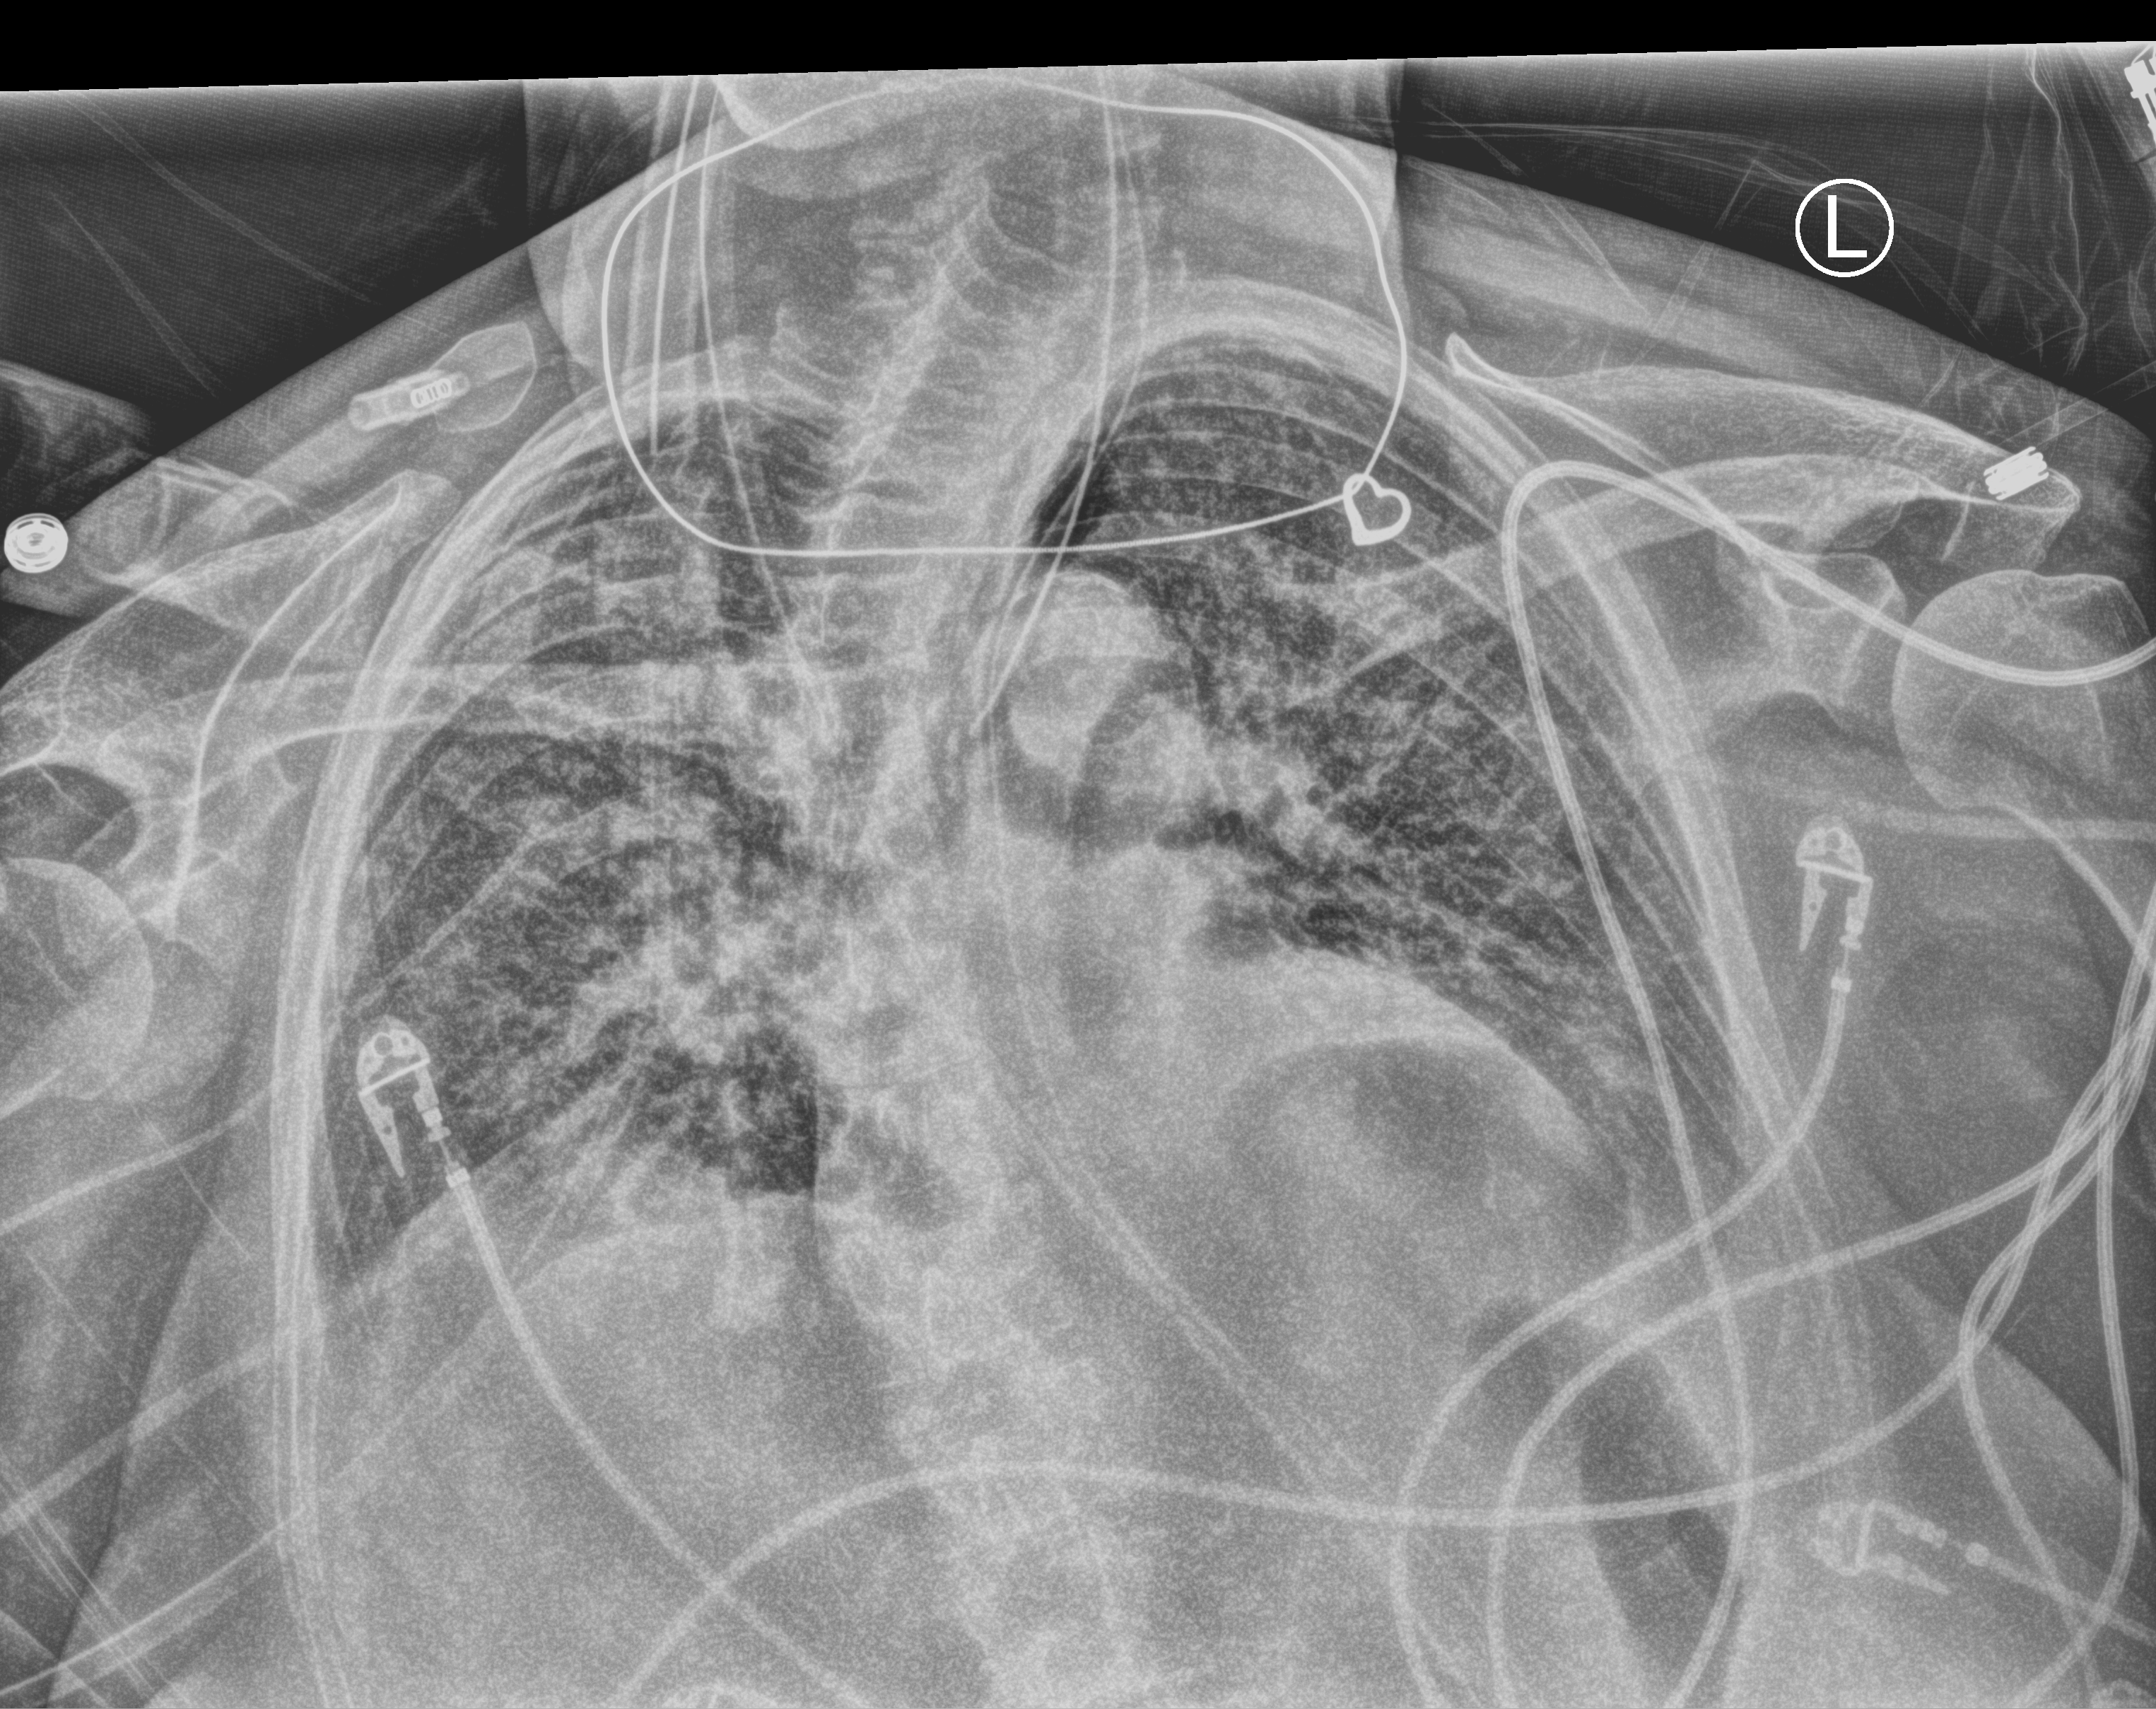
Chest X-ray (portable). Patient hospitalised with COVID-19; female, aged 75–90 years.
Admission-level facts for this patient (not findings on this image; timing relative to this image not recorded): mechanically ventilated during this hospital stay: yes.